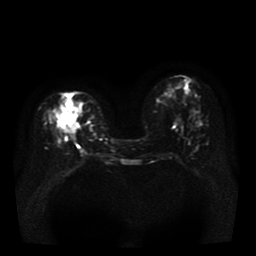
Breast MRI, one axial slice; position 16 of 41 along the scan axis; diffusion-weighted series; image 2 of 4 stored at this slice position (different b-values; order by instance number); 1.5 T; 5 mm slice thickness; 256 × 256 image matrix. Female patient.
Annotated regions visible in this slice (manually delineated by an expert):
- tumour on diffusion-weighted imaging: bounding box (x1, y1, x2, y2) in pixels: (59, 101, 80, 134)